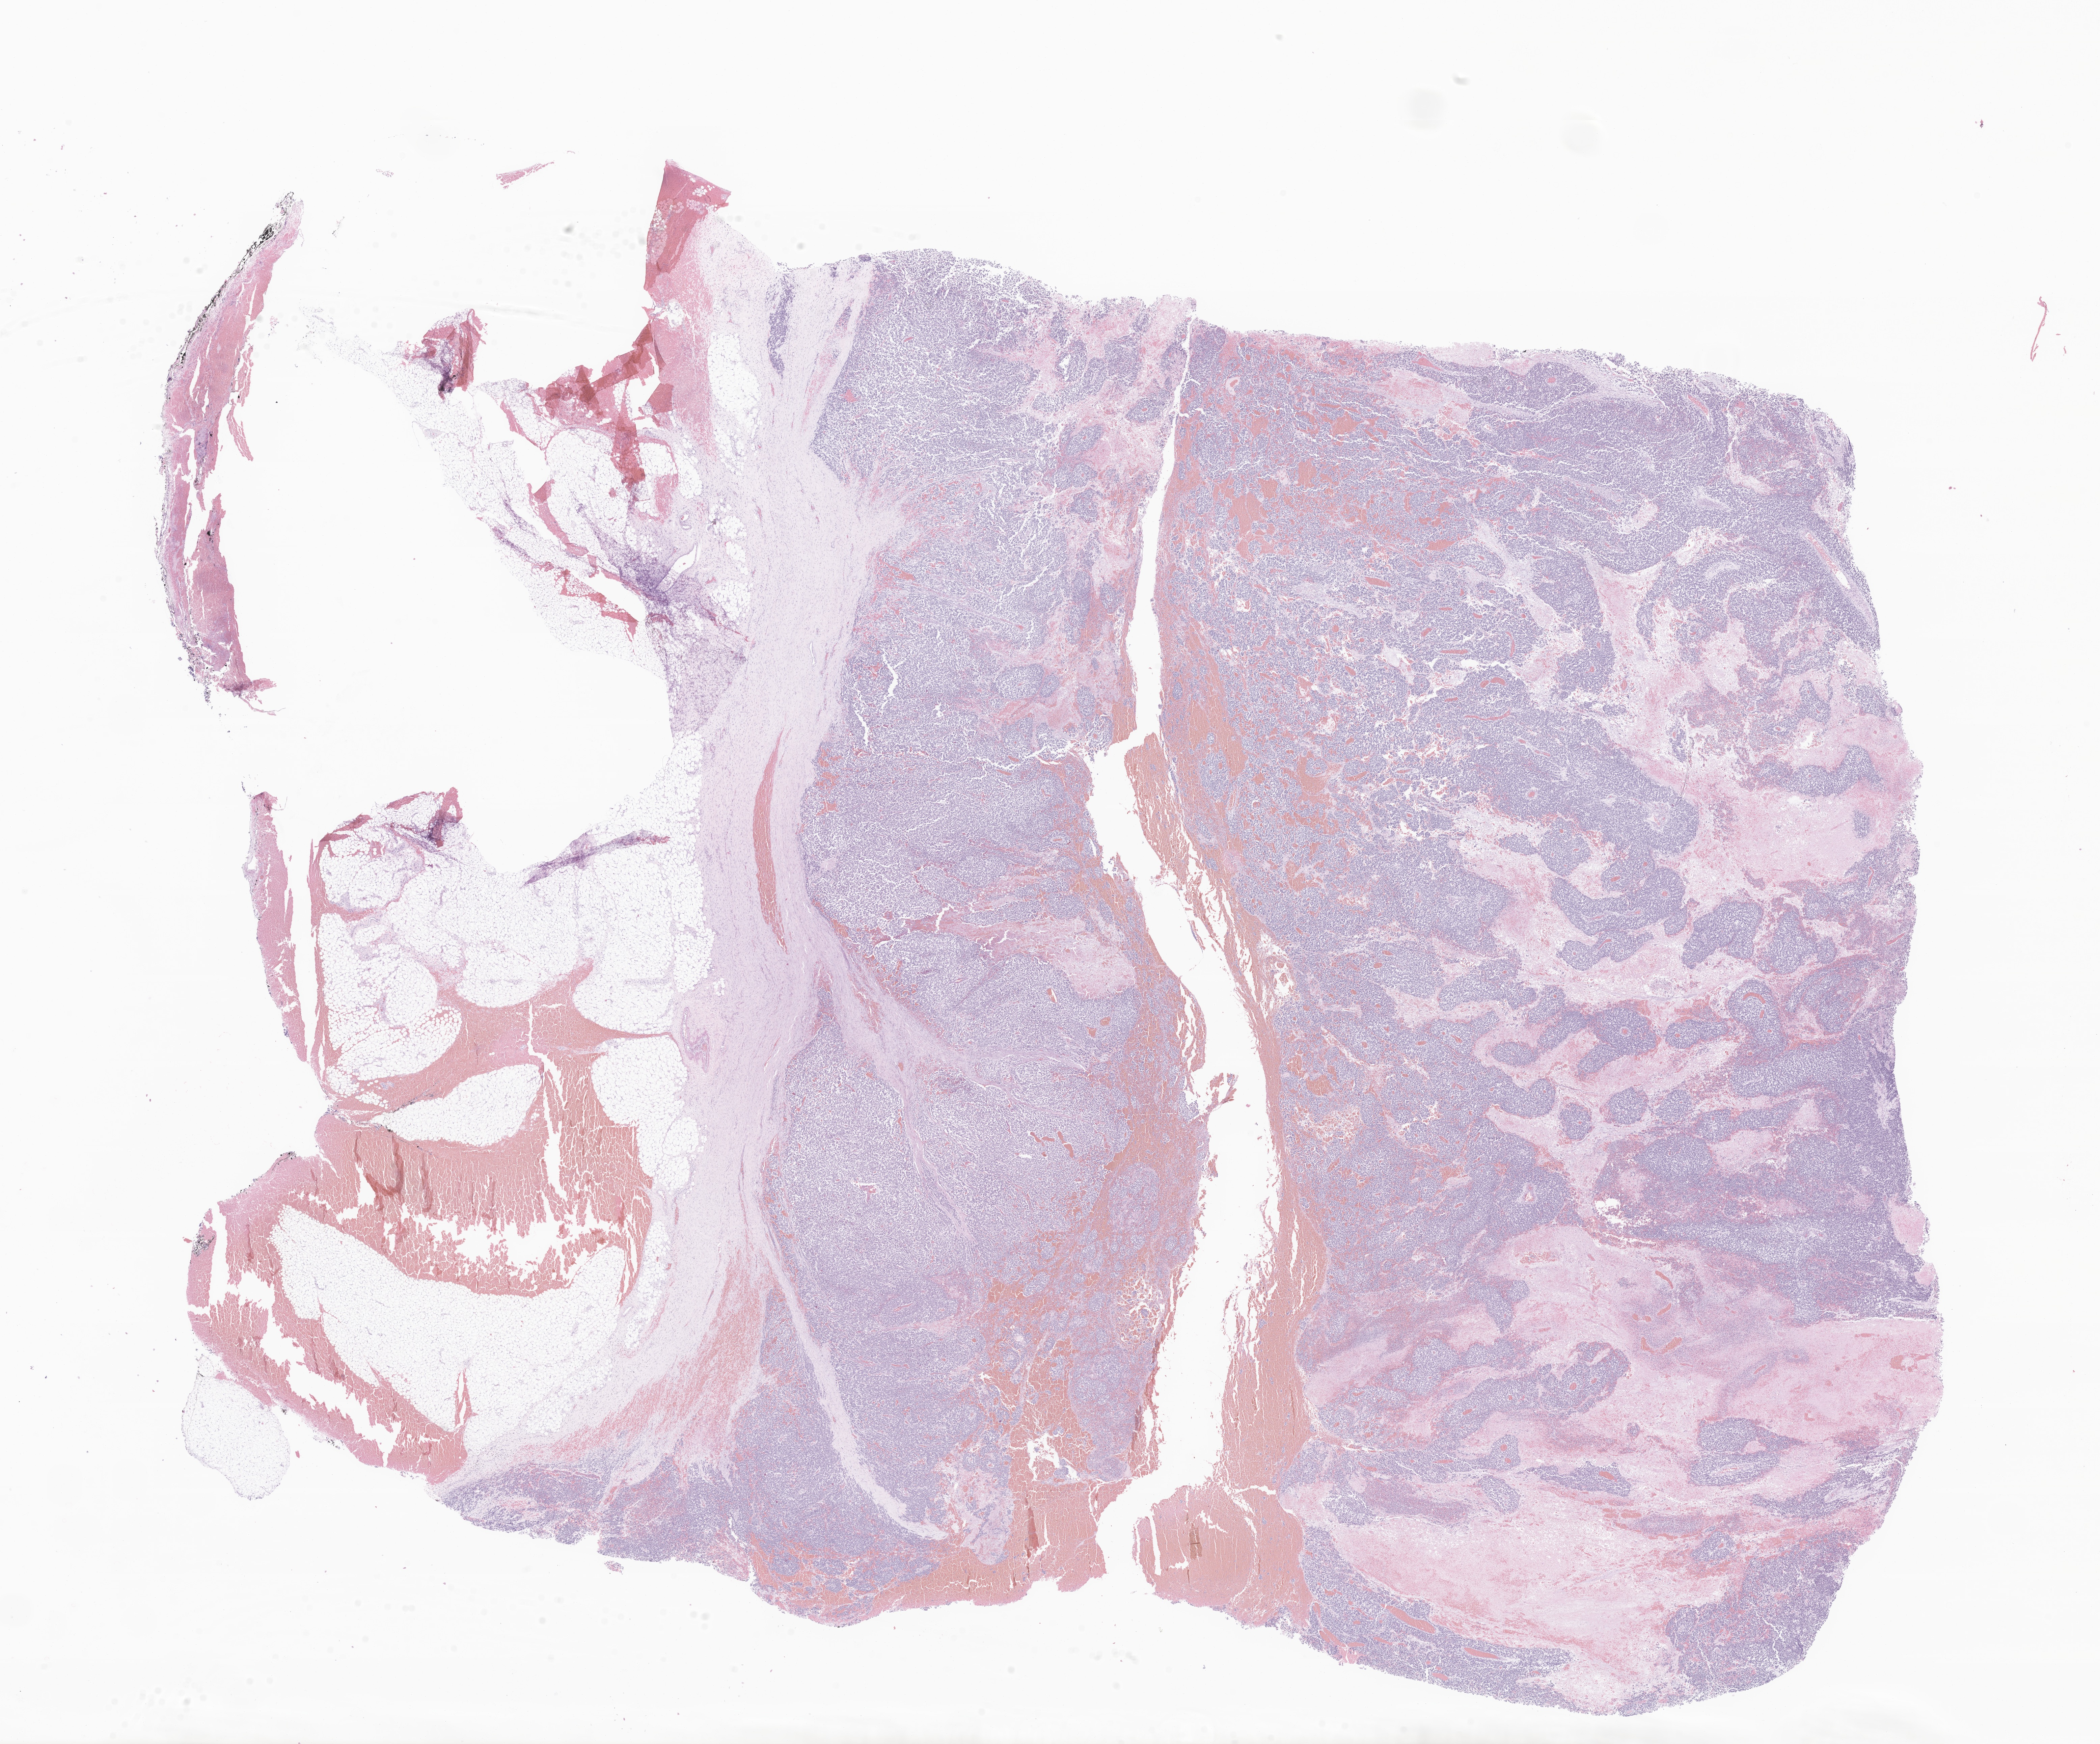
Digitized H&E-stained section of tumor tissue from the kidney, shown as a low-resolution overview of the whole scanned area (about 26.2 x 21.8 mm). Formalin-fixed, paraffin-embedded (FFPE) tissue. Male patient, age 68 months (5 years 8 months).
Diagnosis: Neuroblastoma, NOS.